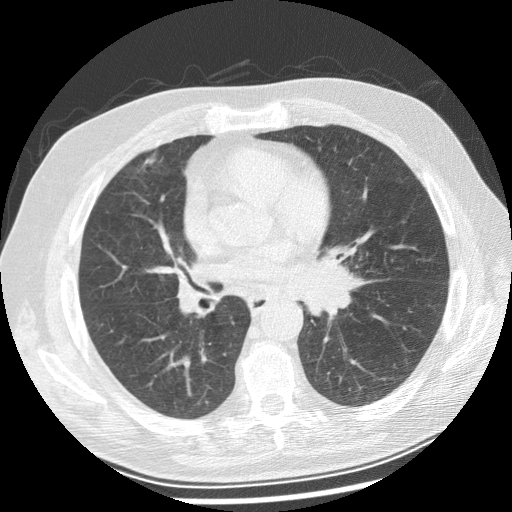
Low-dose screening chest CT, one axial slice; lung window (W 1500 / L -600 HU); 512 × 512 image matrix, field of view 360 × 360 mm.
Annotated regions visible in this slice (outlined manually by an expert reader):
- lesion 1 (tumor, left main bronchus): bounding box <294,259,366,318> (left, top, right, bottom; pixels)